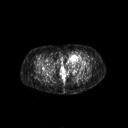
FDG PET of an extremity soft-tissue mass (from a PET/CT study), one axial slice. Slice 42 of 267 in the series (ordered by position). 3.27 mm slice thickness. 128 × 128 image matrix, field of view 700 × 700 mm. Female patient, age 47 years. From the clinical record (not read from this slice): histological type: myxofibrosarcoma; grade: intermediate; site of the primary tumour: left thigh.
Outlined on this slice (expert contour drawn on MRI and transferred to this co-registered scan by the dataset authors):
- gross tumour volume including surrounding oedema: bounding box <65,54,83,64> (left, top, right, bottom; pixels)
- gross tumour volume (mass): <68,54,79,61>